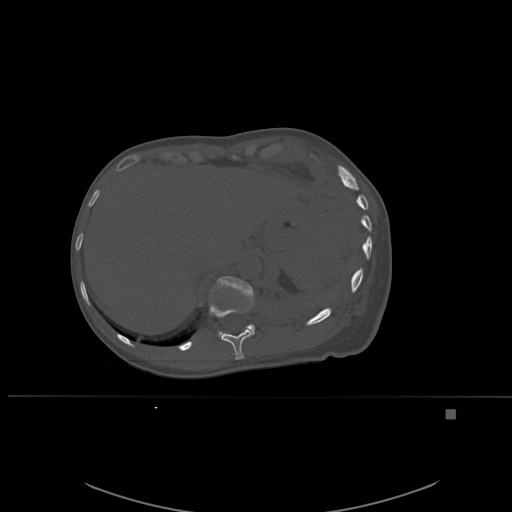
CT including the spine, one axial slice; slice 293 of 537 in the series (ordered by position); bone window (W 1800 / L 400 HU); 1.5 mm slice thickness; 512 × 512 image matrix. Female patient, age 45 years. From the clinical record (not read from this slice): primary cancer: lung.
Outlined on this slice (semi-automatic segmentation, software-assisted and operator-edited):
- T11 vertebra: bounding box <209,290,254,360> (left, top, right, bottom; pixels)
- T12 vertebra: <214,276,255,335>